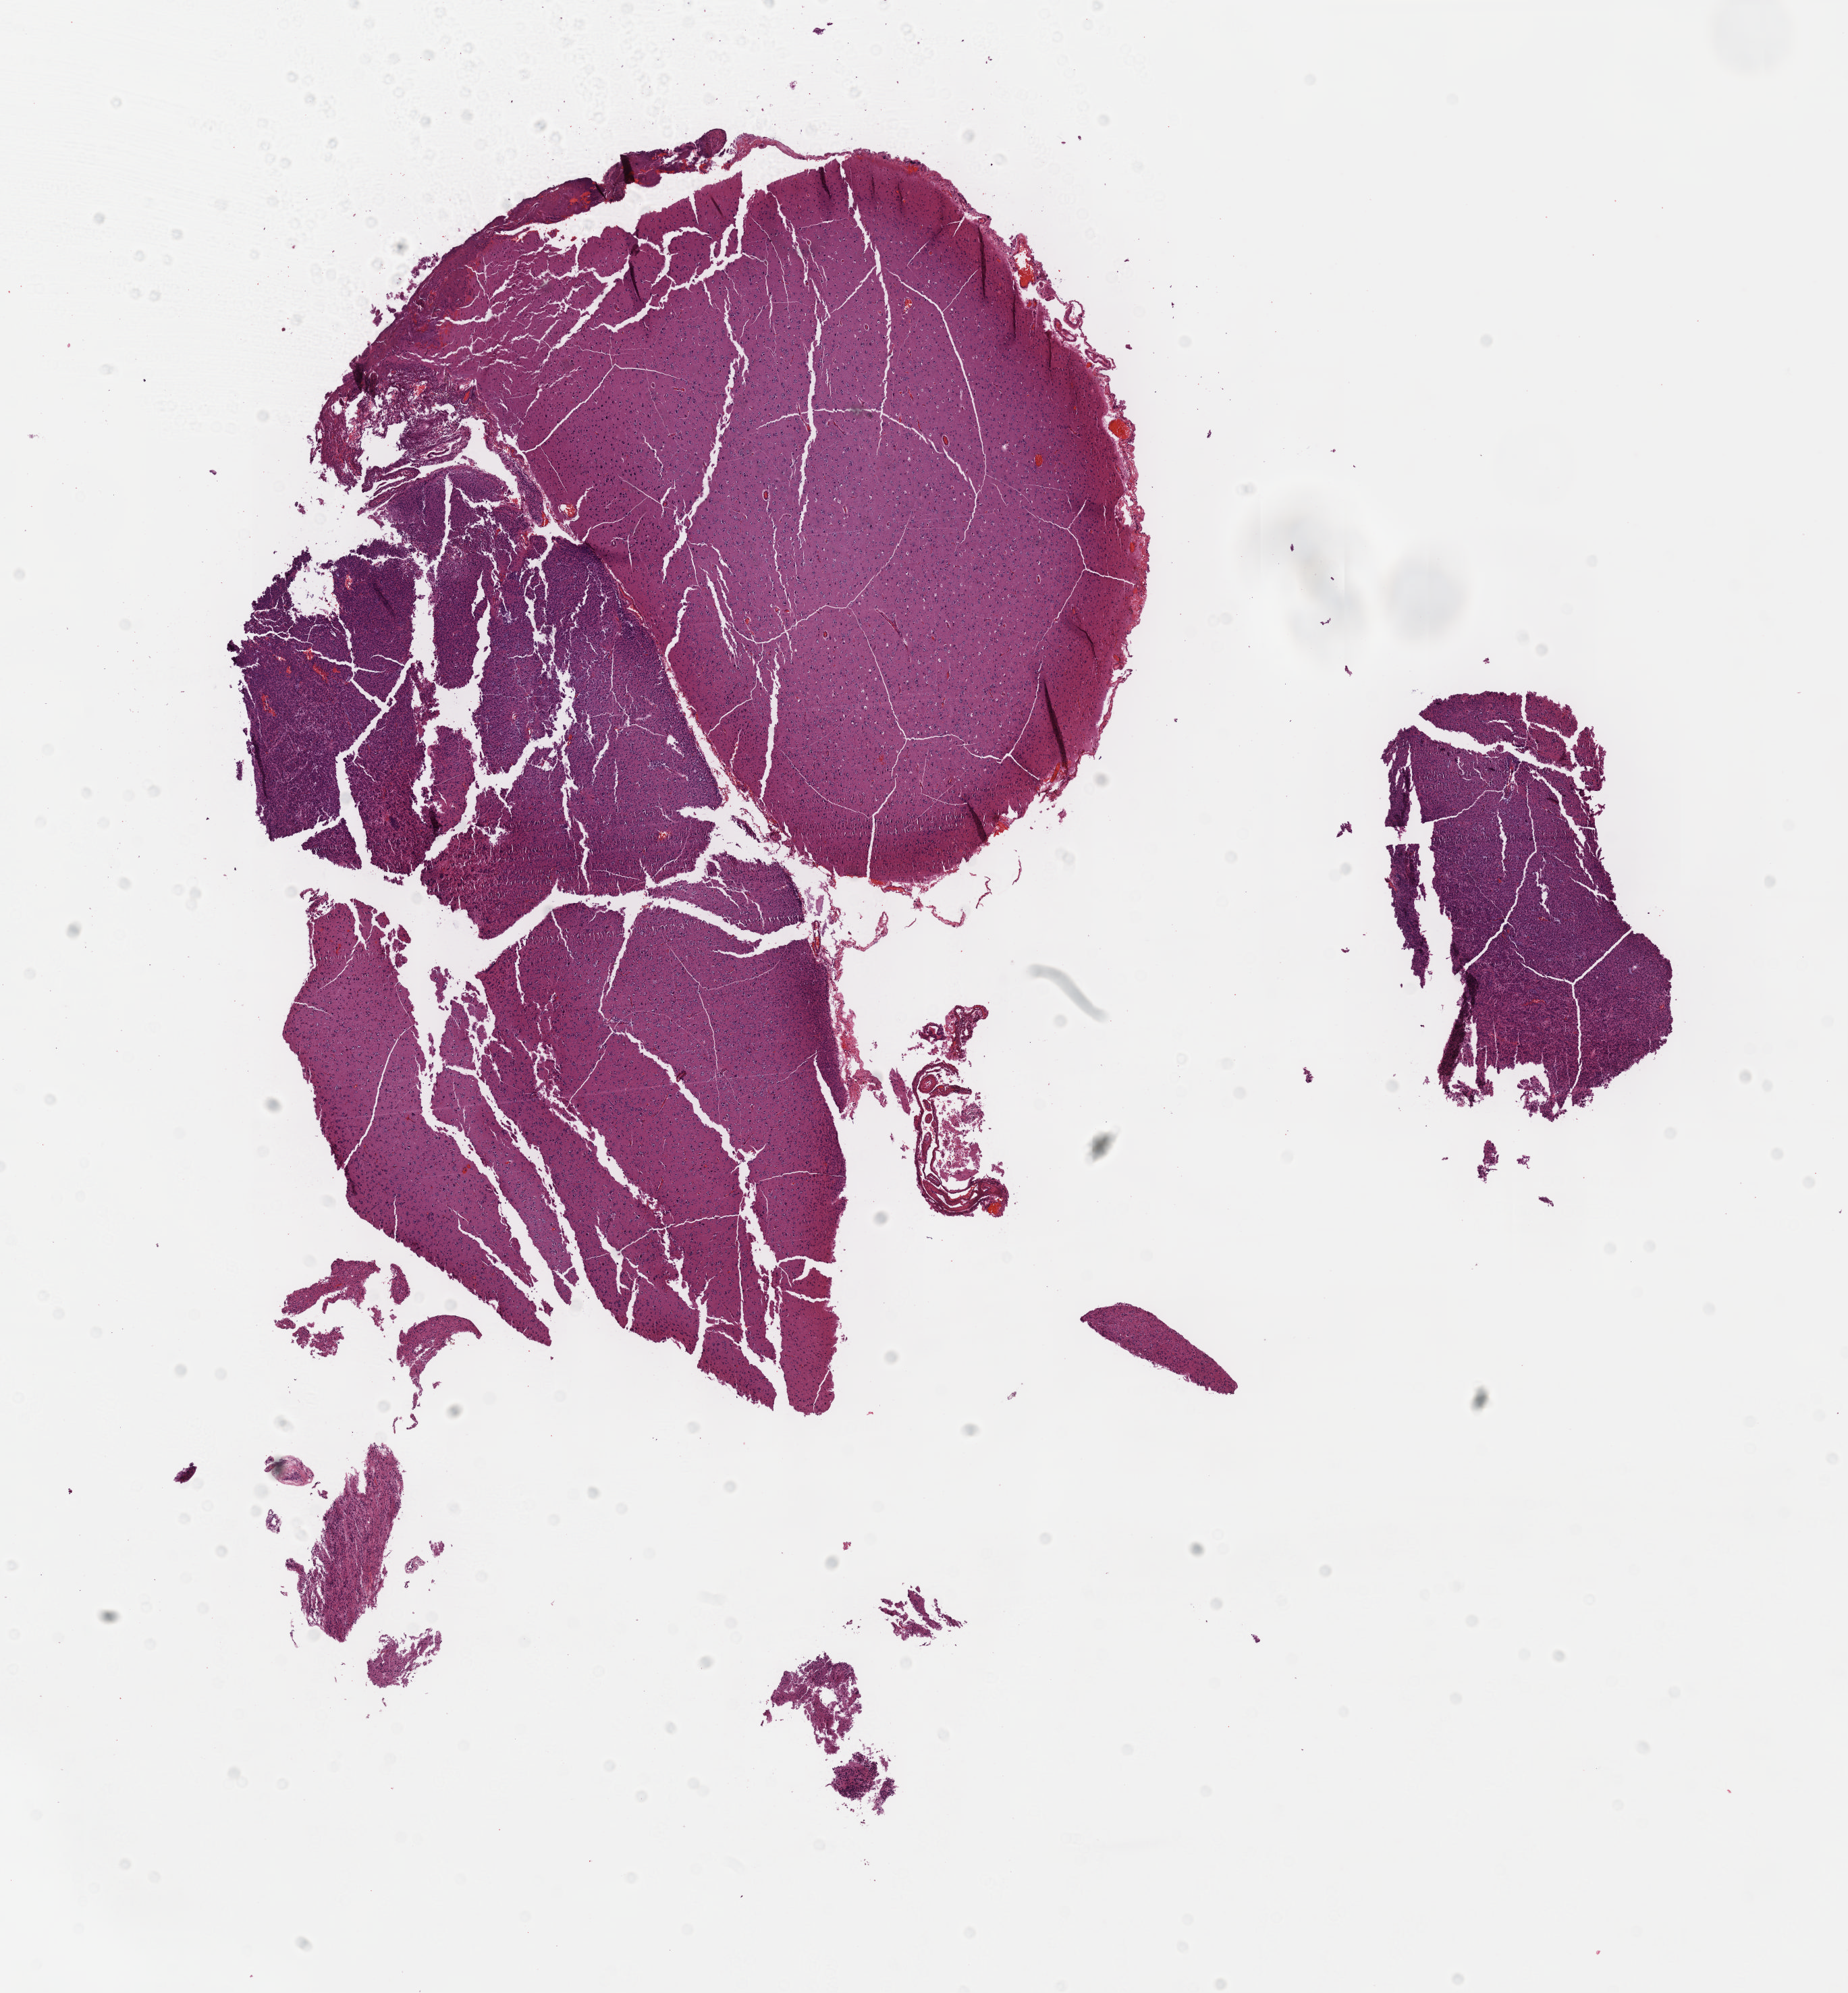
H&E-stained whole-slide image — shown as a low-resolution overview of the whole scanned area (about 11.1 x 11.9 mm), FFPE section, brain, primary tumour sample. Male patient; age at initial diagnosis 39 years. Histologic grade: G2 (moderately differentiated).
Histologic diagnosis: Oligodendroglioma, NOS. Laterality: right.